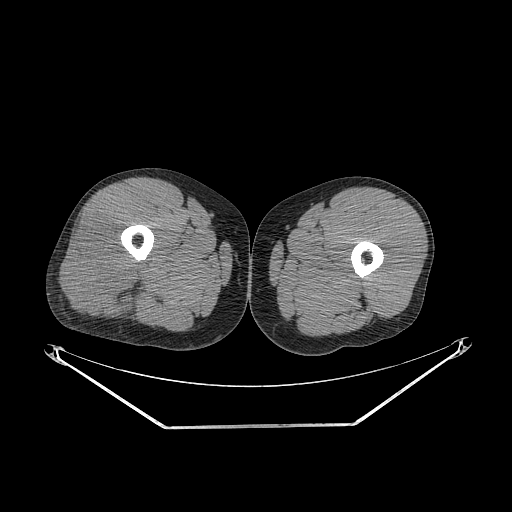
CT of an extremity soft-tissue mass (from a PET/CT study), one axial slice; position 249 of 267 along the scan axis; reconstruction kernel STANDARD; 140 kVp; soft-tissue window (W 400 / L 40 HU); 3.75 mm slice thickness; 512 × 512 image matrix. Male patient. From the clinical record (not read from this slice): histological type: poorly differentiated synovial sarcoma; grade: high; site of the primary tumour: right buttock.
Annotated regions visible in this slice (expert contour drawn on MRI and transferred to this co-registered scan by the dataset authors):
- gross tumour volume including surrounding oedema: box from (x=60, y=219) to (x=143, y=316) px
- gross tumour volume (mass): (x=60, y=221)–(x=140, y=316)